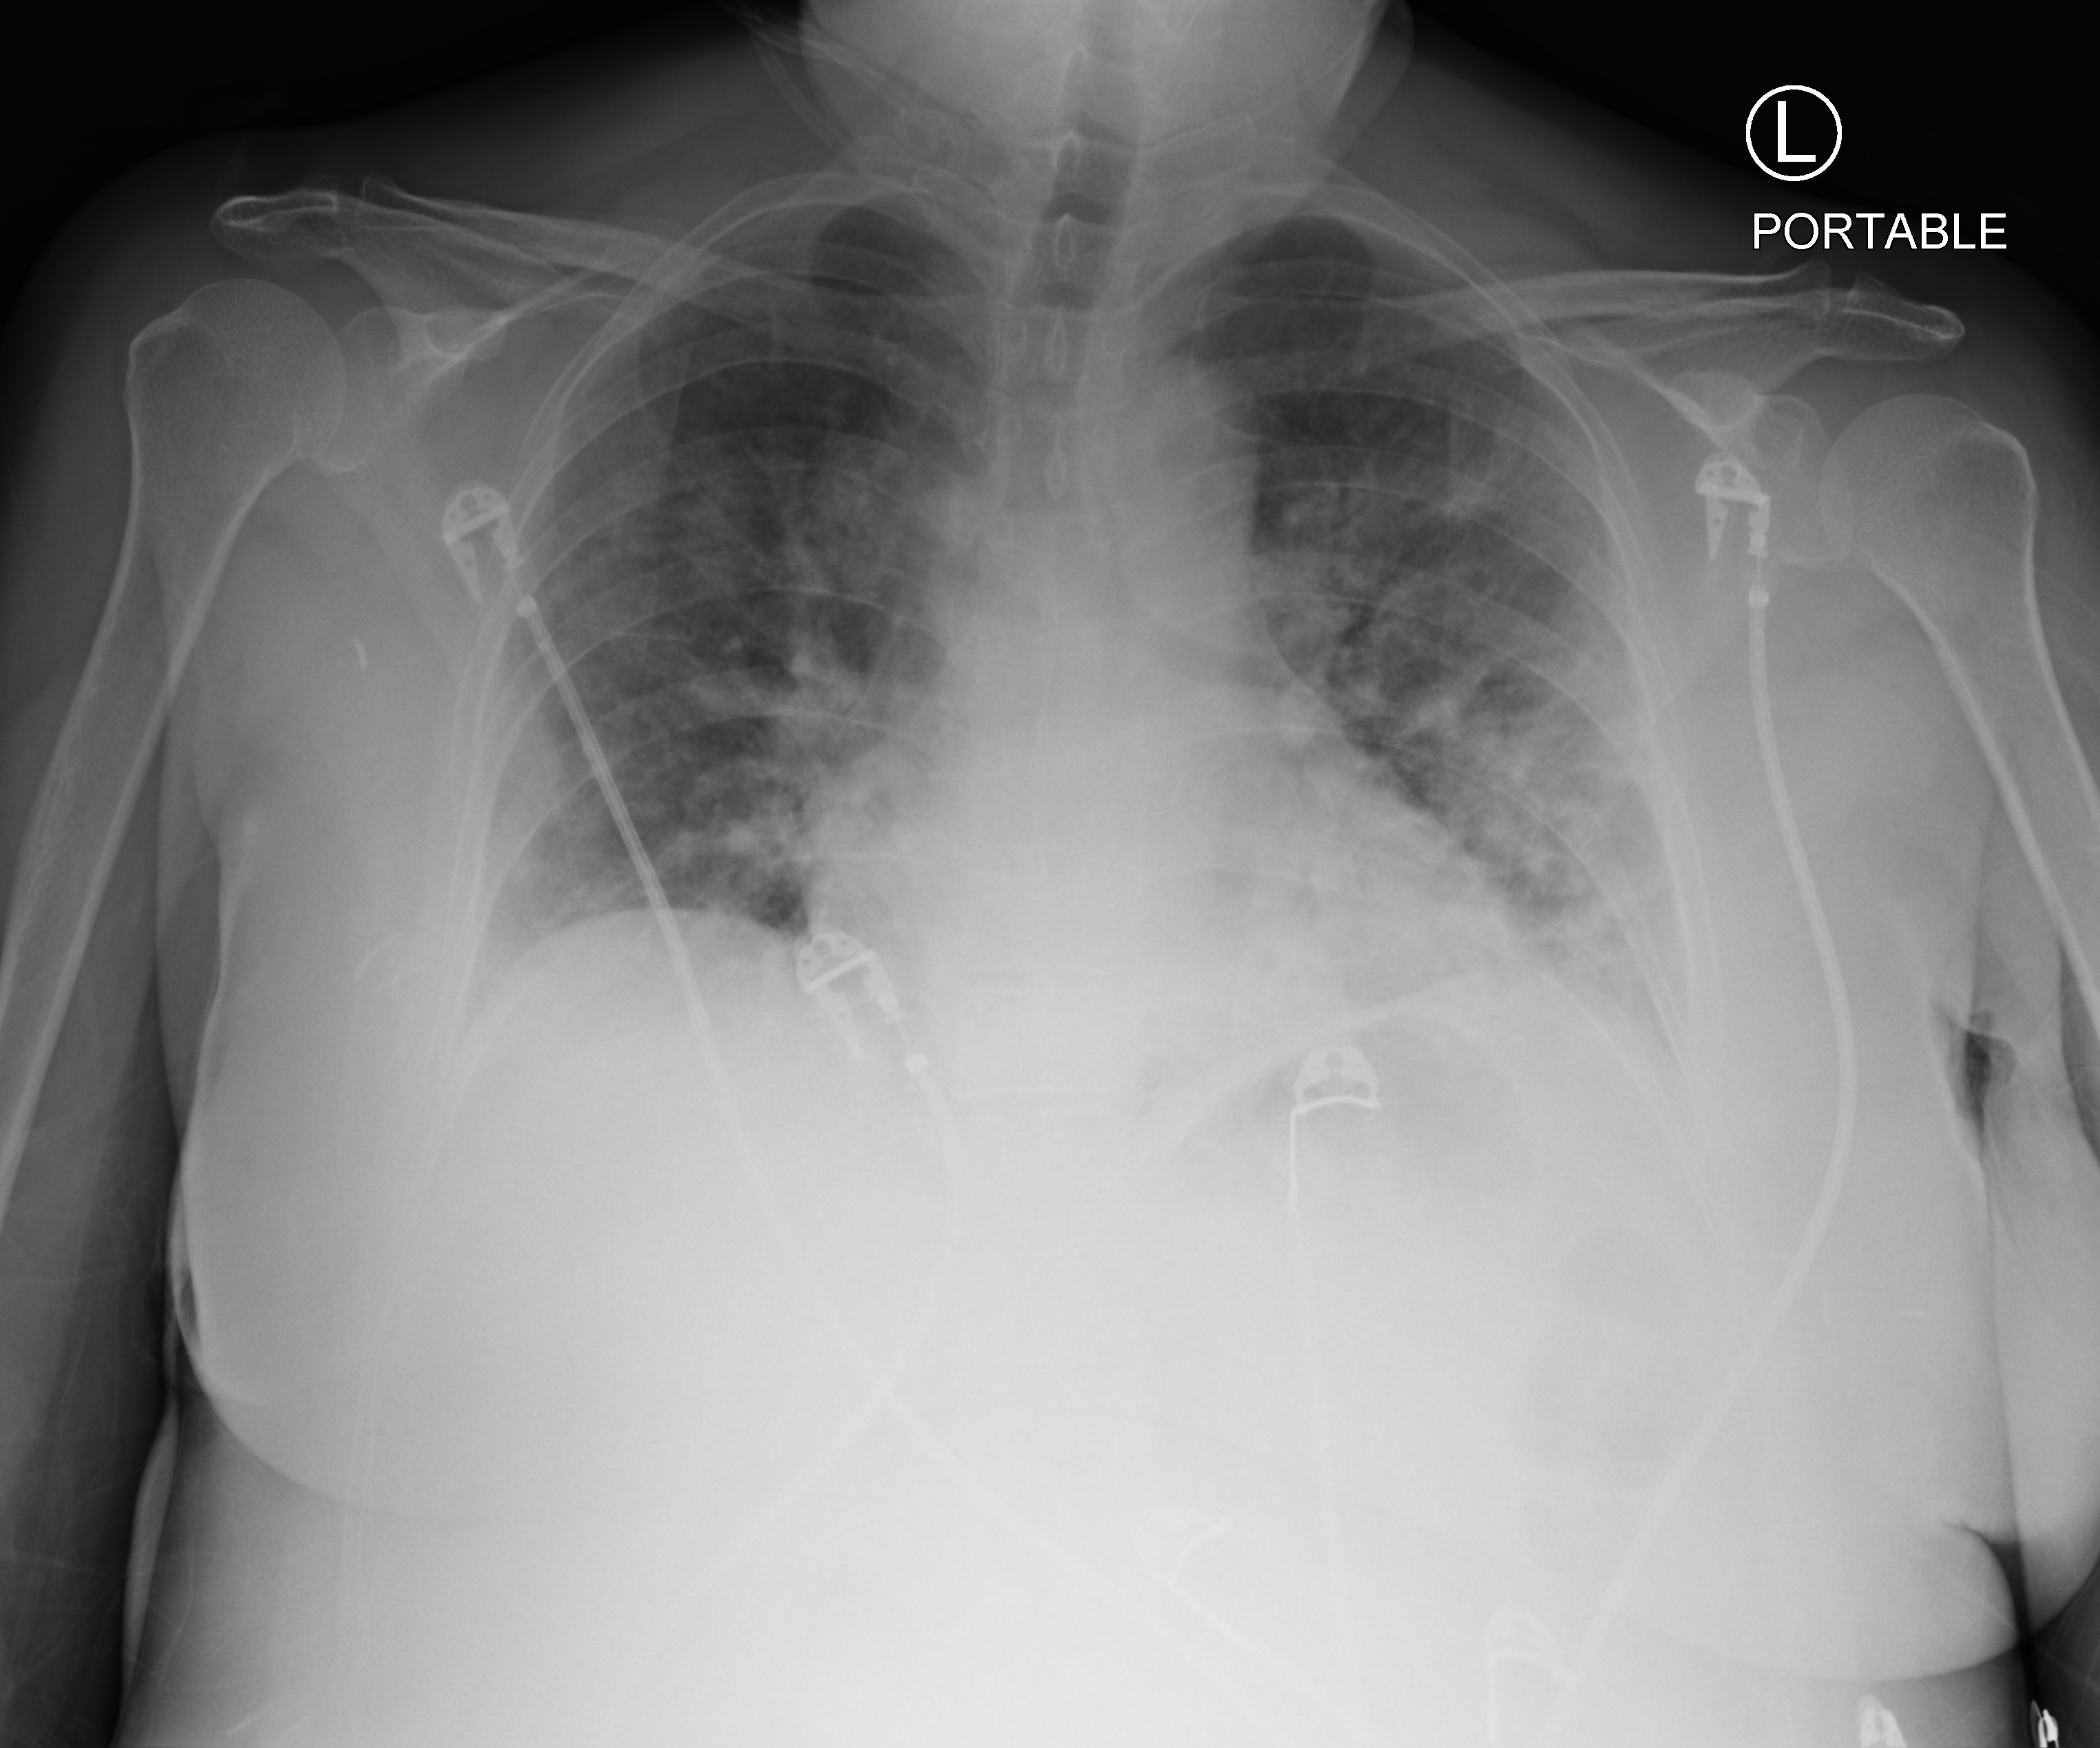
Chest X-ray (portable), anteroposterior (AP) projection. Female patient hospitalised with COVID-19, age 18–59 years.
Admission-level facts for this patient (not findings on this image; timing relative to this image not recorded): admitted to intensive care during this hospital stay: no; mechanically ventilated during this hospital stay: yes.